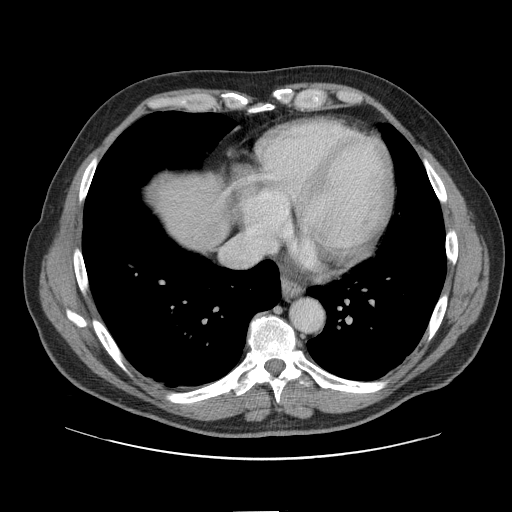
Contrast-enhanced abdominal CT, one axial slice. Position 142 of 161 along the scan axis. Intravenous contrast given. Soft-tissue window (W 400 / L 40 HU). 2.5 mm slice thickness. 512 × 512 image matrix, field of view 412 × 412 mm. Male patient, age 66 years. From the clinical record (not read from this slice): diagnosis: colorectal cancer liver metastases, imaged before liver resection; multiple liver metastases: no; largest metastasis: 3.5 cm; disease in both lobes: no.
Annotated regions visible in this slice (expert manual segmentation):
- hepatic veins: bounding box [x1, y1, x2, y2] px = [225, 241, 237, 254]
- liver: [158, 178, 230, 250]
- planned liver remnant (the part of the liver to remain after resection): [158, 178, 228, 250]
- liver metastasis: [212, 191, 217, 203]